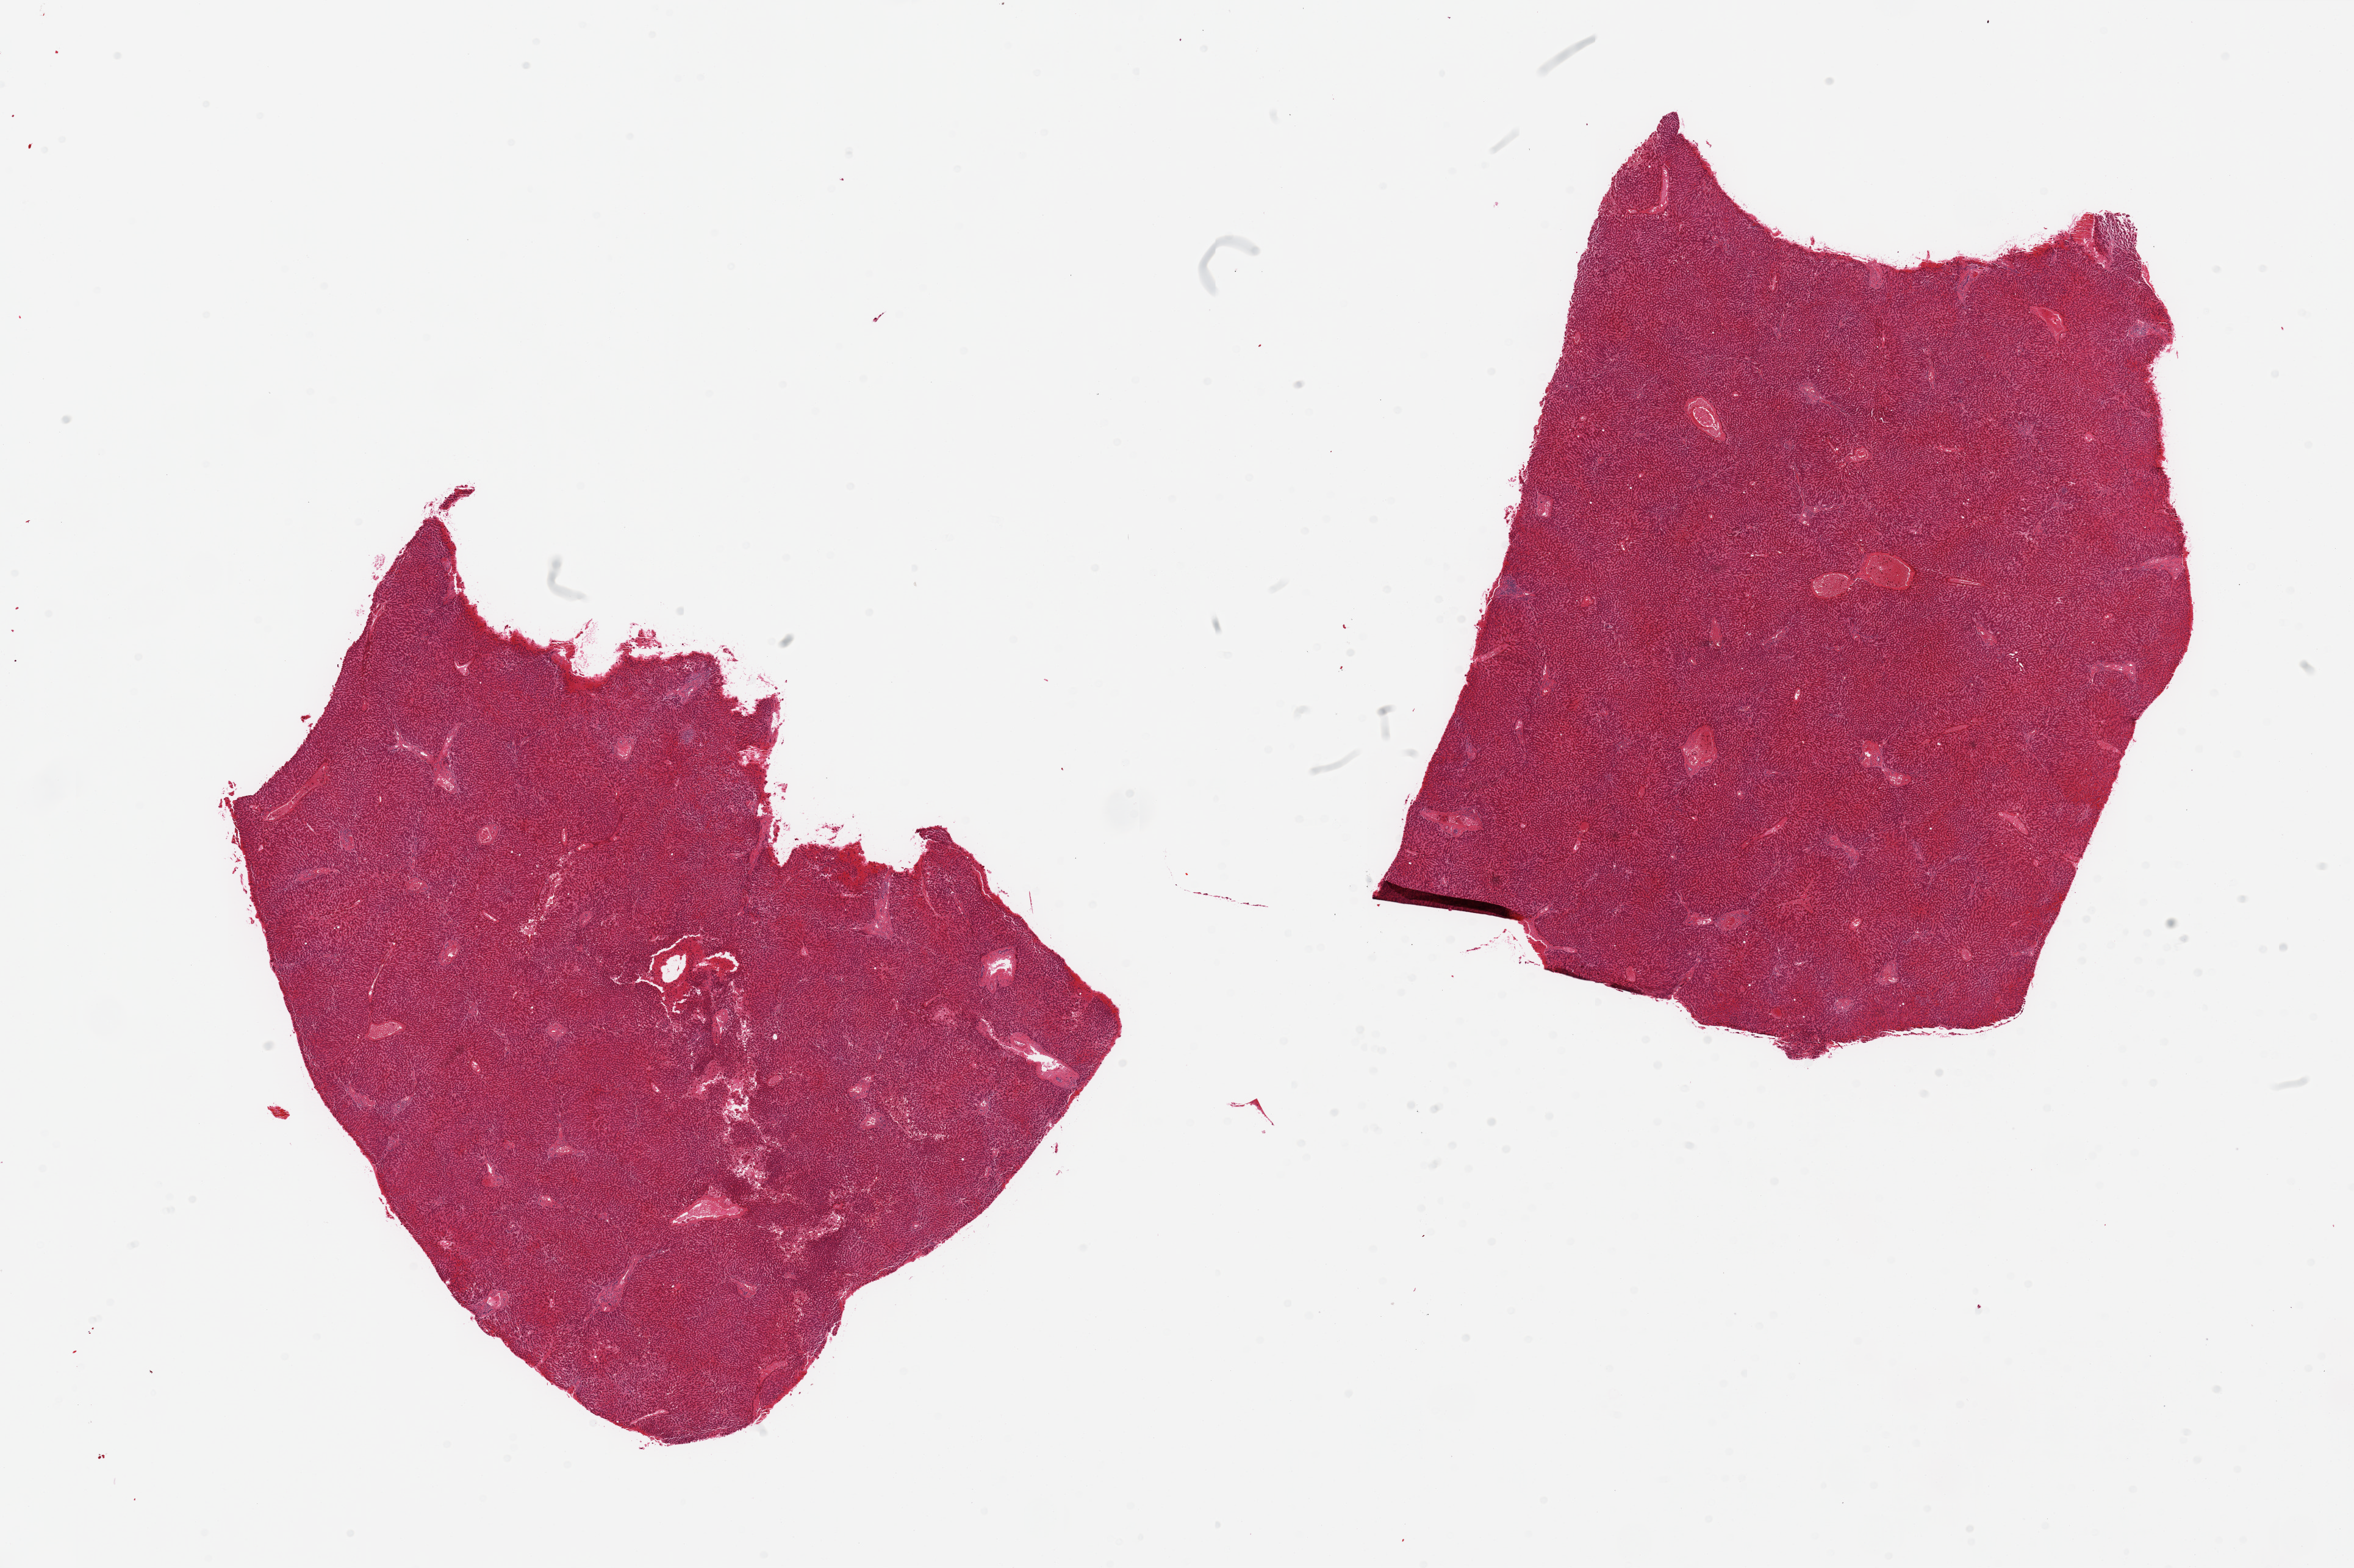
Digitized H&E-stained section, brightfield, a low-resolution overview of the entire scanned area, about 30.5 x 20.3 mm; PAXgene-fixed paraffin-embedded (PFPE) section; section of liver (target tissue); donor tissue sample. Donor: male.
Review note (as recorded): 2 pieces; moderate passive congestion.